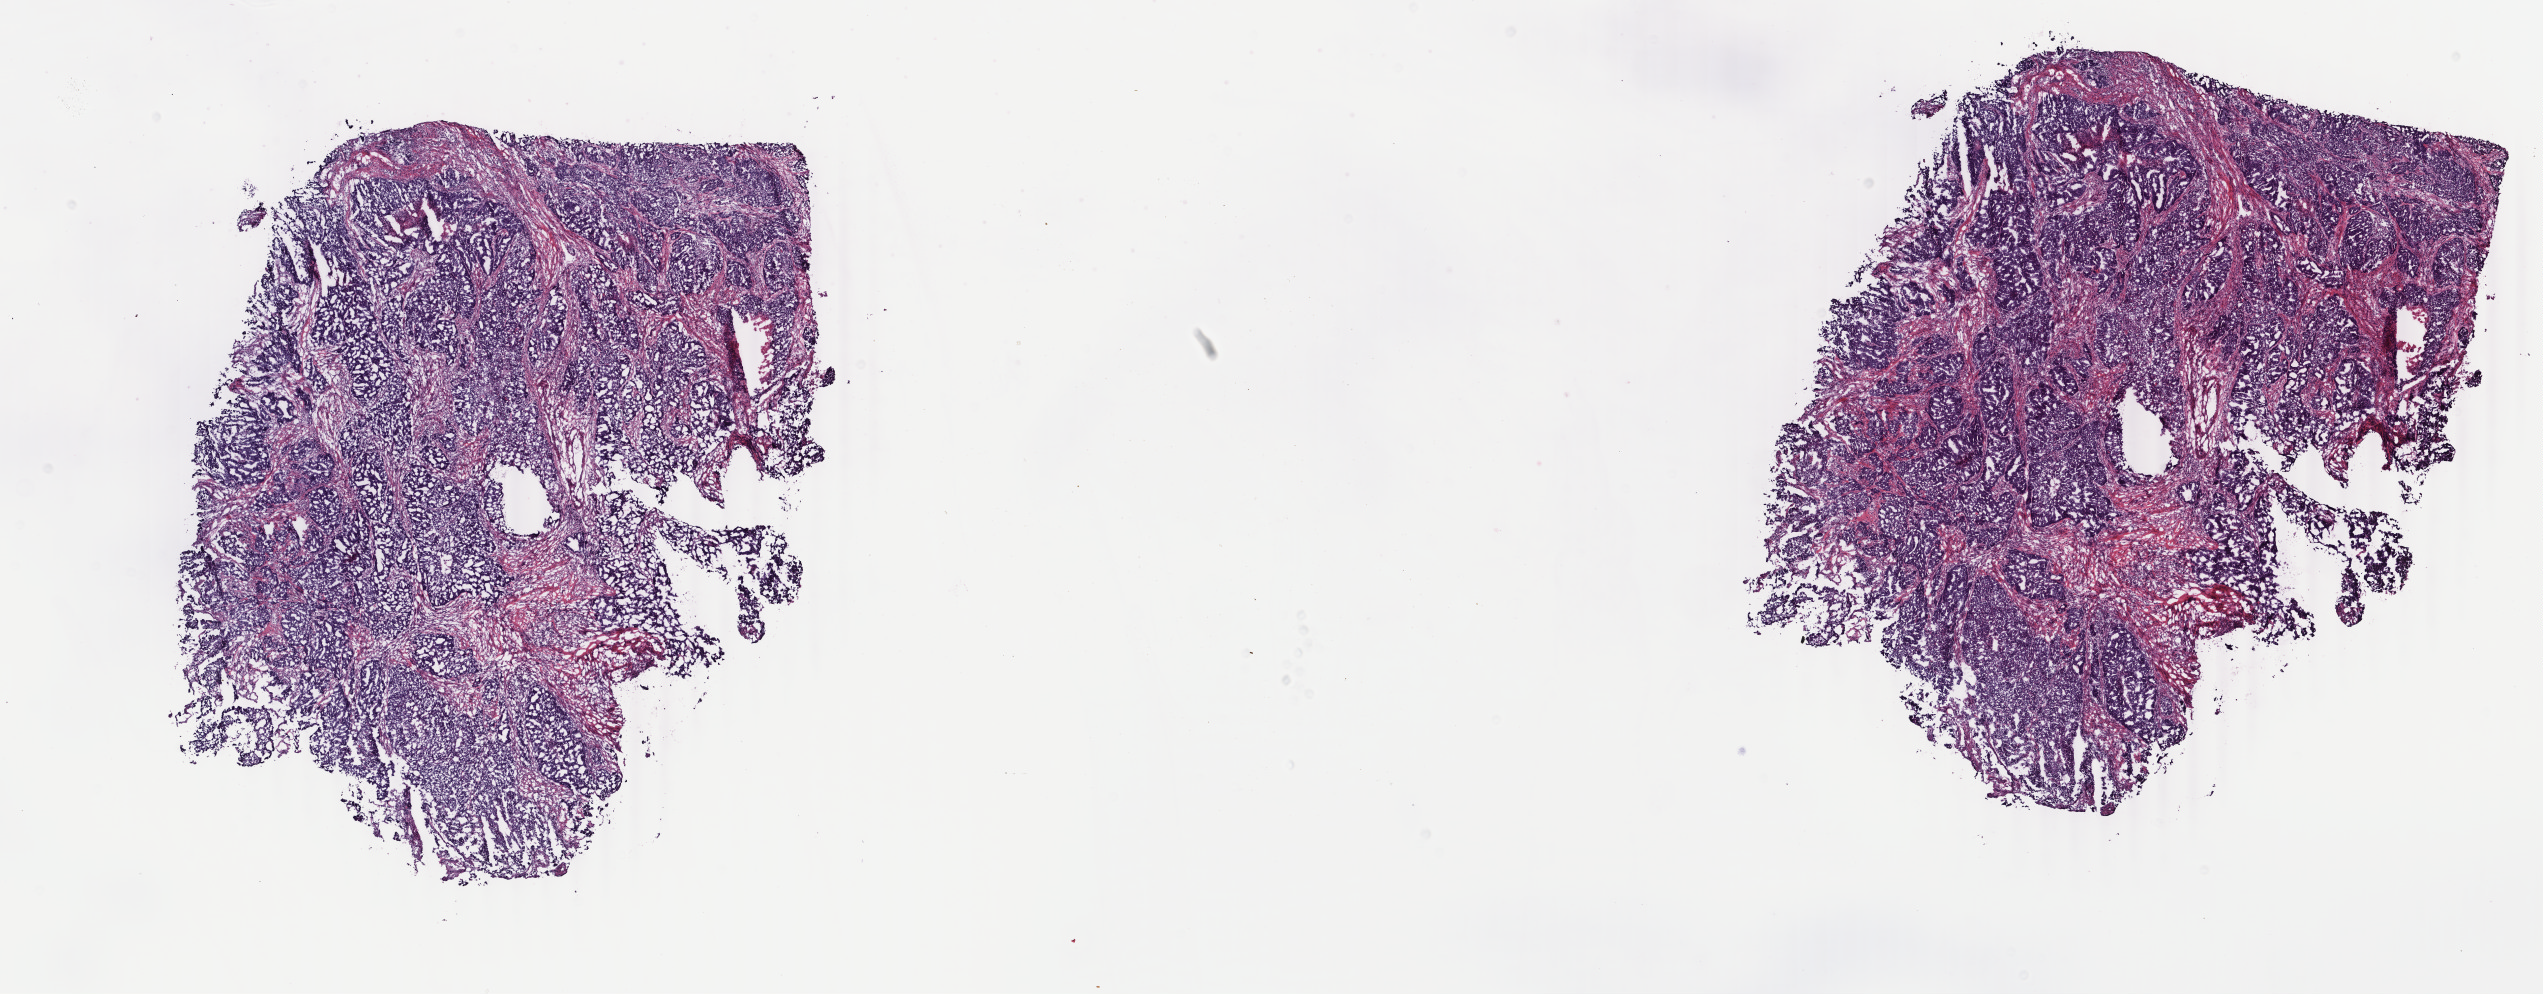
Hematoxylin and eosin (H&E) stained whole-slide image, low-resolution overview of the scanned area, about 20.2 x 7.9 mm (from a 40x scan). Frozen section from the top of the tissue portion. Primary tumour sample from the uterus. Female, age 73 years at initial diagnosis.
Diagnosis: Endometrioid adenocarcinoma, NOS.